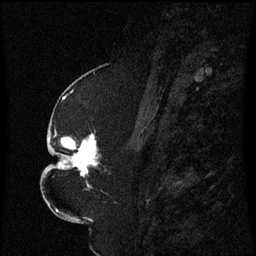
Breast MRI (dynamic contrast-enhanced), one sagittal slice. Position 31 of 60 along the scan axis. Dynamic contrast-enhanced series, image 2 of 3 at this slice position (ordered by acquisition). 1.5 T. TE 4.2 ms, TR 8.4 ms. 2.3 mm slice thickness. 256 × 256 image matrix, field of view 200 × 200 mm. Patient: female, 52 years. From the clinical record (not read from this slice): setting: breast cancer imaged before/during neoadjuvant chemotherapy; receptor status: HR-positive, HER2-negative.
Structures marked on this image (semi-automatically segmented with operator editing):
- analysis volume of interest (the breast-tissue region the enhancement analysis was run in; not a lesion): bounding box [x1, y1, x2, y2] px = [49, 124, 111, 191]
- tumour enhancement mask (voxels above the 70 % enhancement threshold inside the analysis volume of interest): [57, 134, 99, 187]